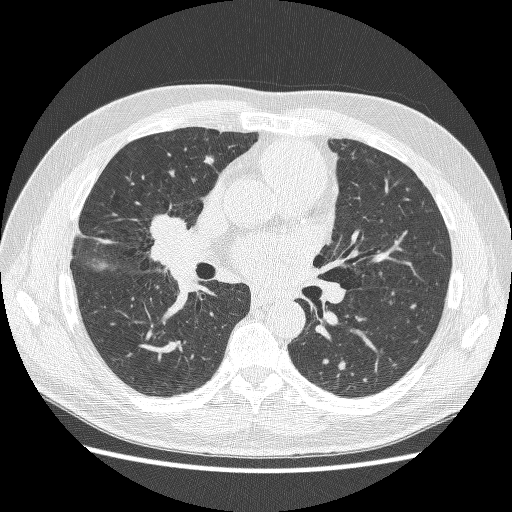
Low-dose screening chest CT, axial slice, baseline annual screen, lung window (W 1500 / L -600 HU), 1.25 mm slice thickness, lung (sharp) reconstruction kernel (BONE), 120 kVp. Male participant, aged 59 years at enrolment. Former smoker at enrolment.
Expert reader's lesion annotation, bounding box (x1, y1, x2, y2) in pixels: (128, 206, 198, 271). No non-calcified nodule or mass ≥4 mm was recorded by the screening reader at this exam. Later outcome: lung cancer diagnosed 24 days after this screen — adenocarcinoma, NOS, right middle lobe, poorly differentiated (G3), stage IV (AJCC 6th edition), 54 mm at pathology.